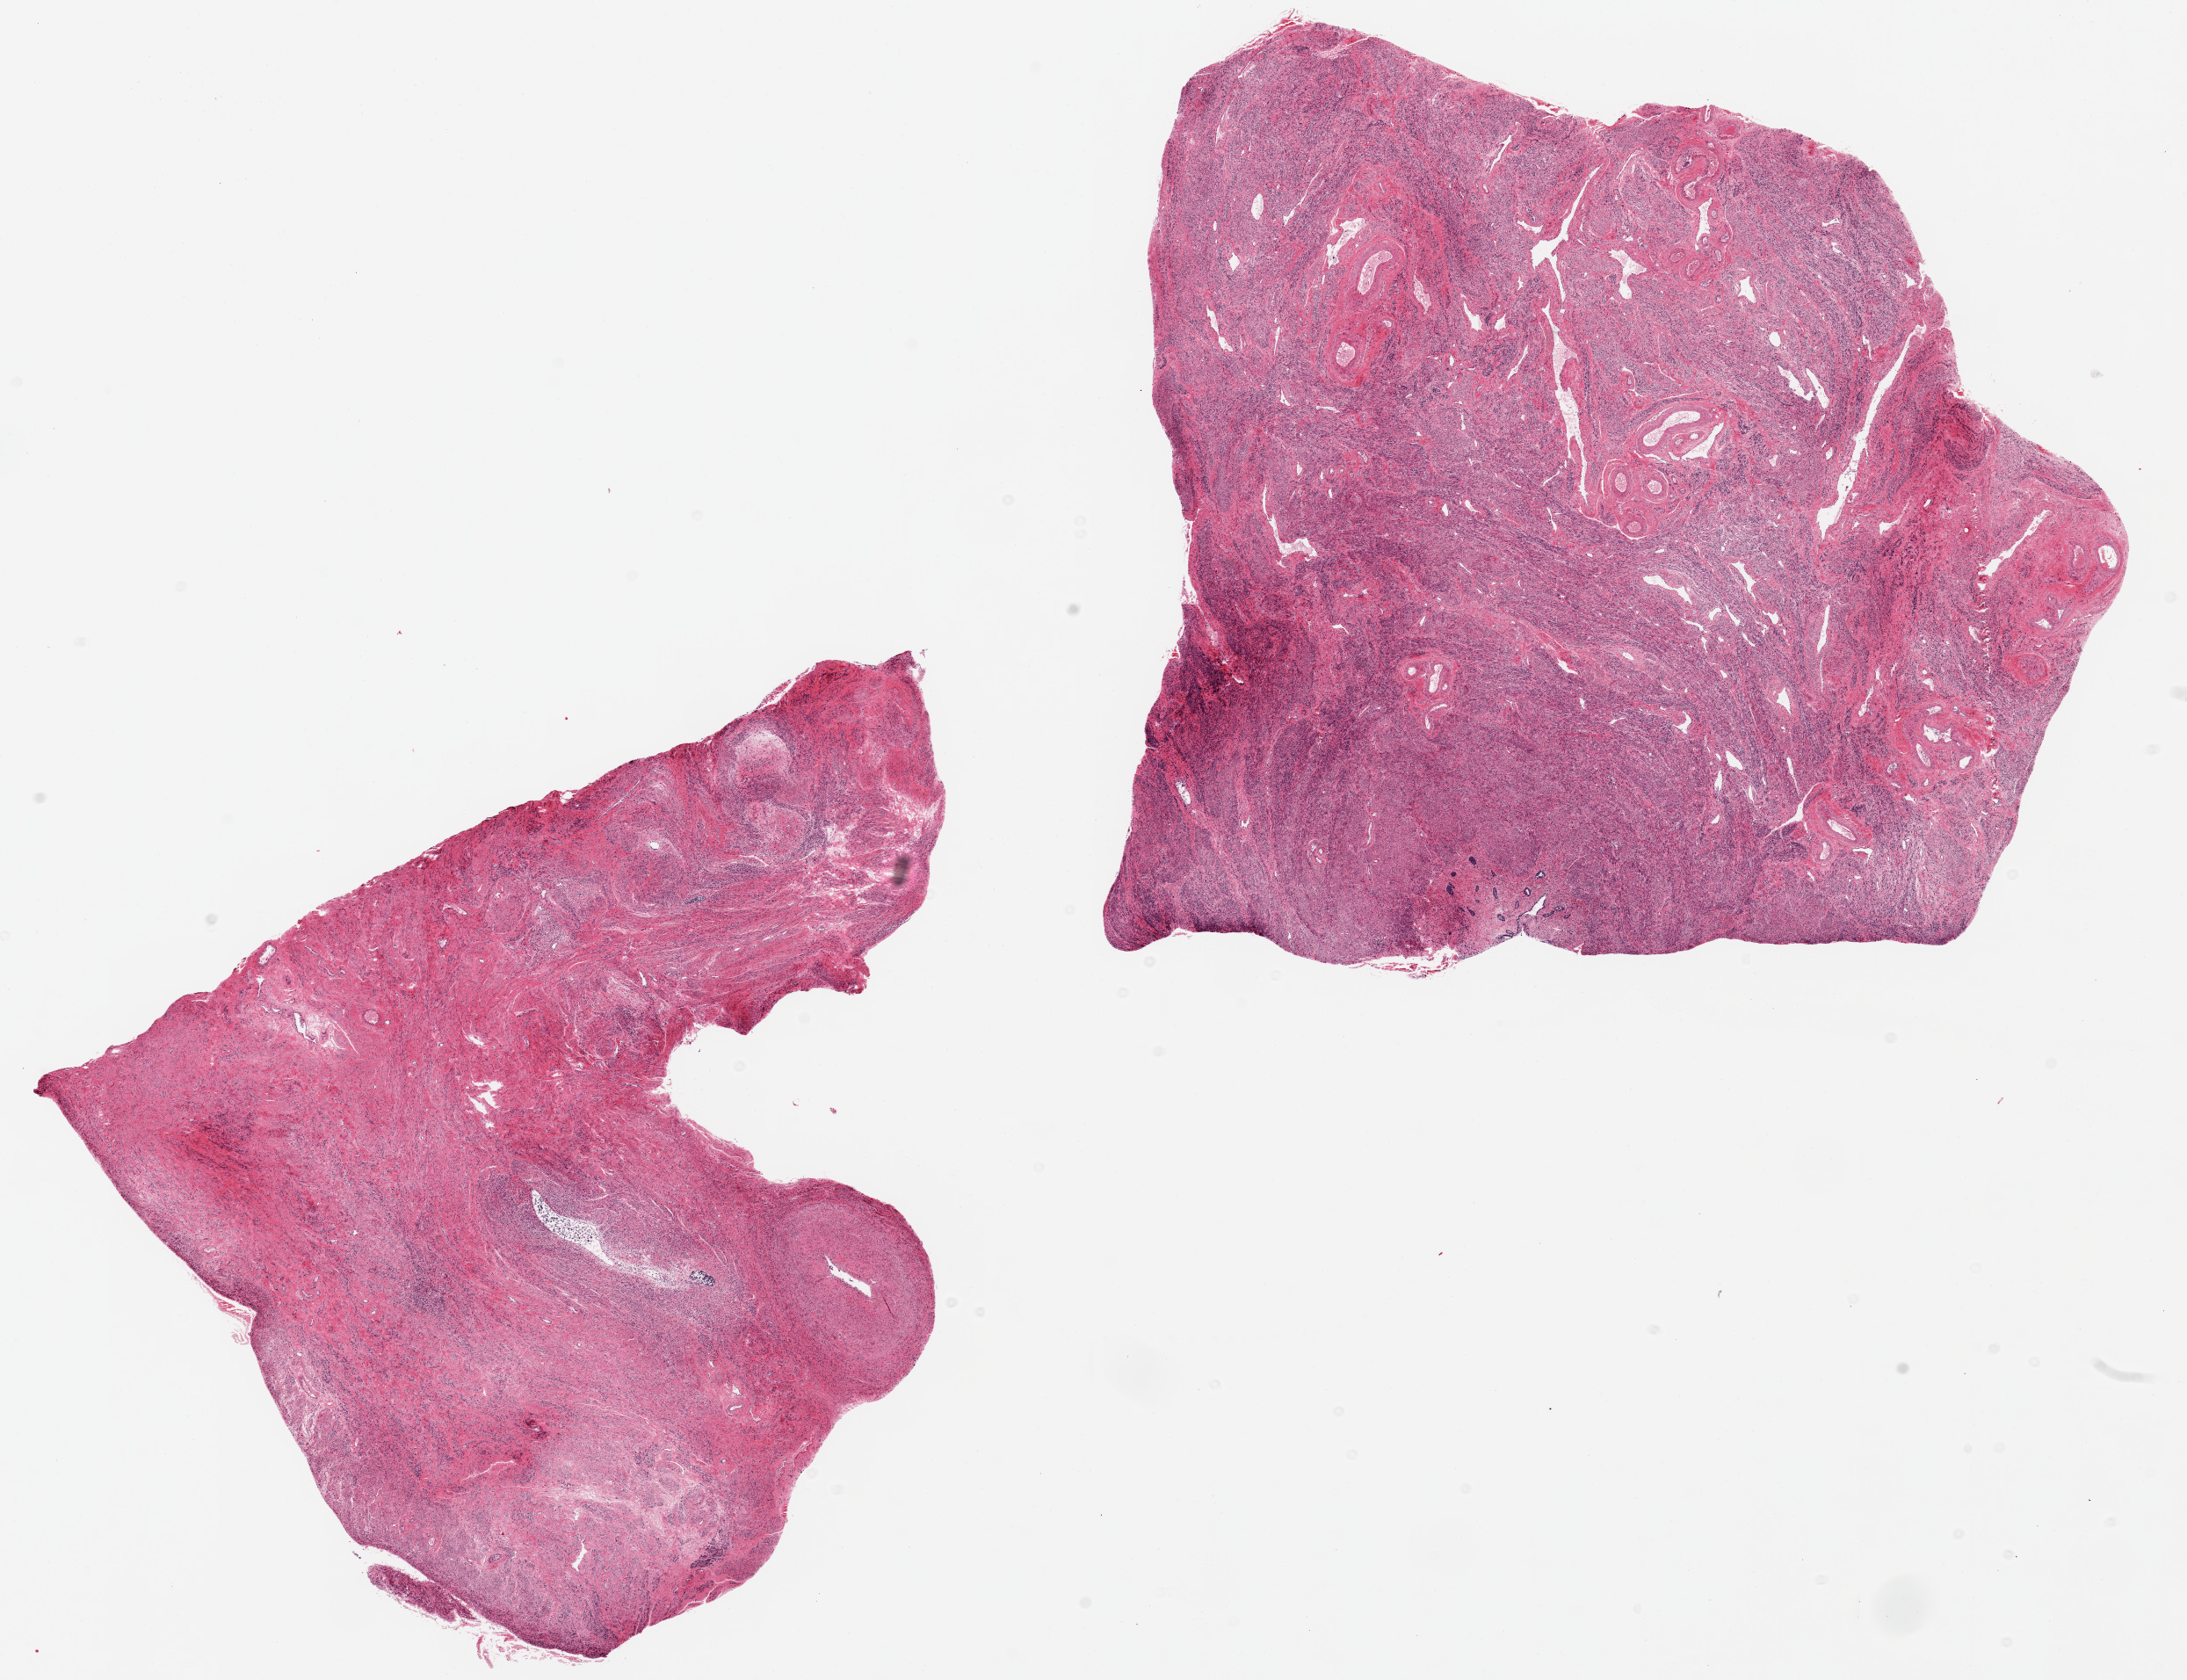
Whole-slide image, haematoxylin and eosin stain, a low-resolution overview of the entire scanned area, about 19.7 x 15.1 mm (from a 20x scan). PAXgene-fixed paraffin-embedded (PFPE) section. Sampled site (target tissue): uterus. Donor tissue sample. Female donor.
Review note (as recorded): 2 pieces; 9x7 & 9.5x9mm; Small (1-2mm) atrophic foci of endometrium (1 autolyzed); Most is myometrium (autolysis=1).